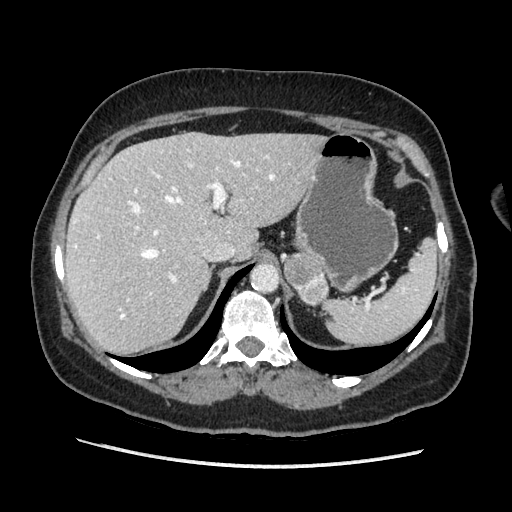
Contrast-enhanced abdominal CT, one axial slice; position 143 of 203 along the scan axis; soft-tissue window (W 400 / L 40 HU); 1.25 mm slice thickness; 512 × 512 image matrix, field of view 360 × 360 mm. Female patient. From the clinical record (not read from this slice): diagnosis: adrenocortical carcinoma; tumour side: left adrenal; tumour size at pathology: 6.5 cm; Ki-67 index: 22 %; stage (as recorded): 2.
Outlined on this slice (semi-automatically segmented with operator editing):
- mass: bounding box <283,254,328,304> (left, top, right, bottom; pixels)